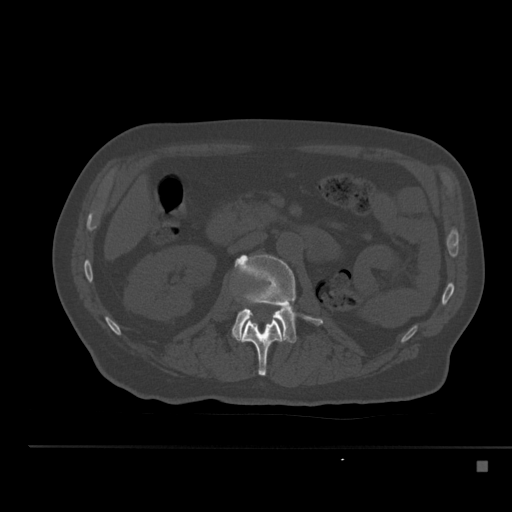
CT including the spine, one axial slice; slice 196 of 517 in the series (ordered by position); reconstruction kernel Br40s; bone window (W 1800 / L 400 HU); 512 × 512 image matrix, field of view 408 × 408 mm. Patient: male, 70 years. From the clinical record (not read from this slice): primary cancer: renal.
Structures marked on this image (semi-automatic segmentation, software-assisted and operator-edited):
- L1 vertebra: bounding box [x1, y1, x2, y2] px = [238, 318, 287, 376]
- L2 vertebra: [232, 254, 323, 343]